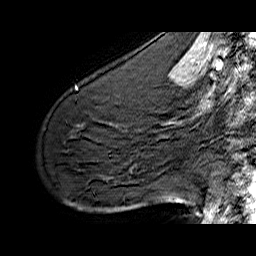
Breast MRI (dynamic contrast-enhanced), one sagittal slice; position 39 of 60 along the scan axis; dynamic contrast-enhanced series, time point 2 of 6 at this slice position (early post-contrast); 1.5 T; TE 6.4 ms, TR 32.9 ms; 4 mm slice thickness; 256 × 256 image matrix, field of view 200 × 200 mm. Female patient. From the clinical record (not read from this slice): setting: breast cancer imaged before/during neoadjuvant chemotherapy; receptor status: HER2-positive.
Structures marked on this image (semi-automatic segmentation, software-assisted and operator-edited):
- analysis volume of interest (the breast-tissue region the enhancement analysis was run in; not a lesion): bounding box <61,77,141,142> (left, top, right, bottom; pixels)
- tumour enhancement mask (voxels above the 100 % enhancement threshold inside the analysis volume of interest): <76,87,78,89>